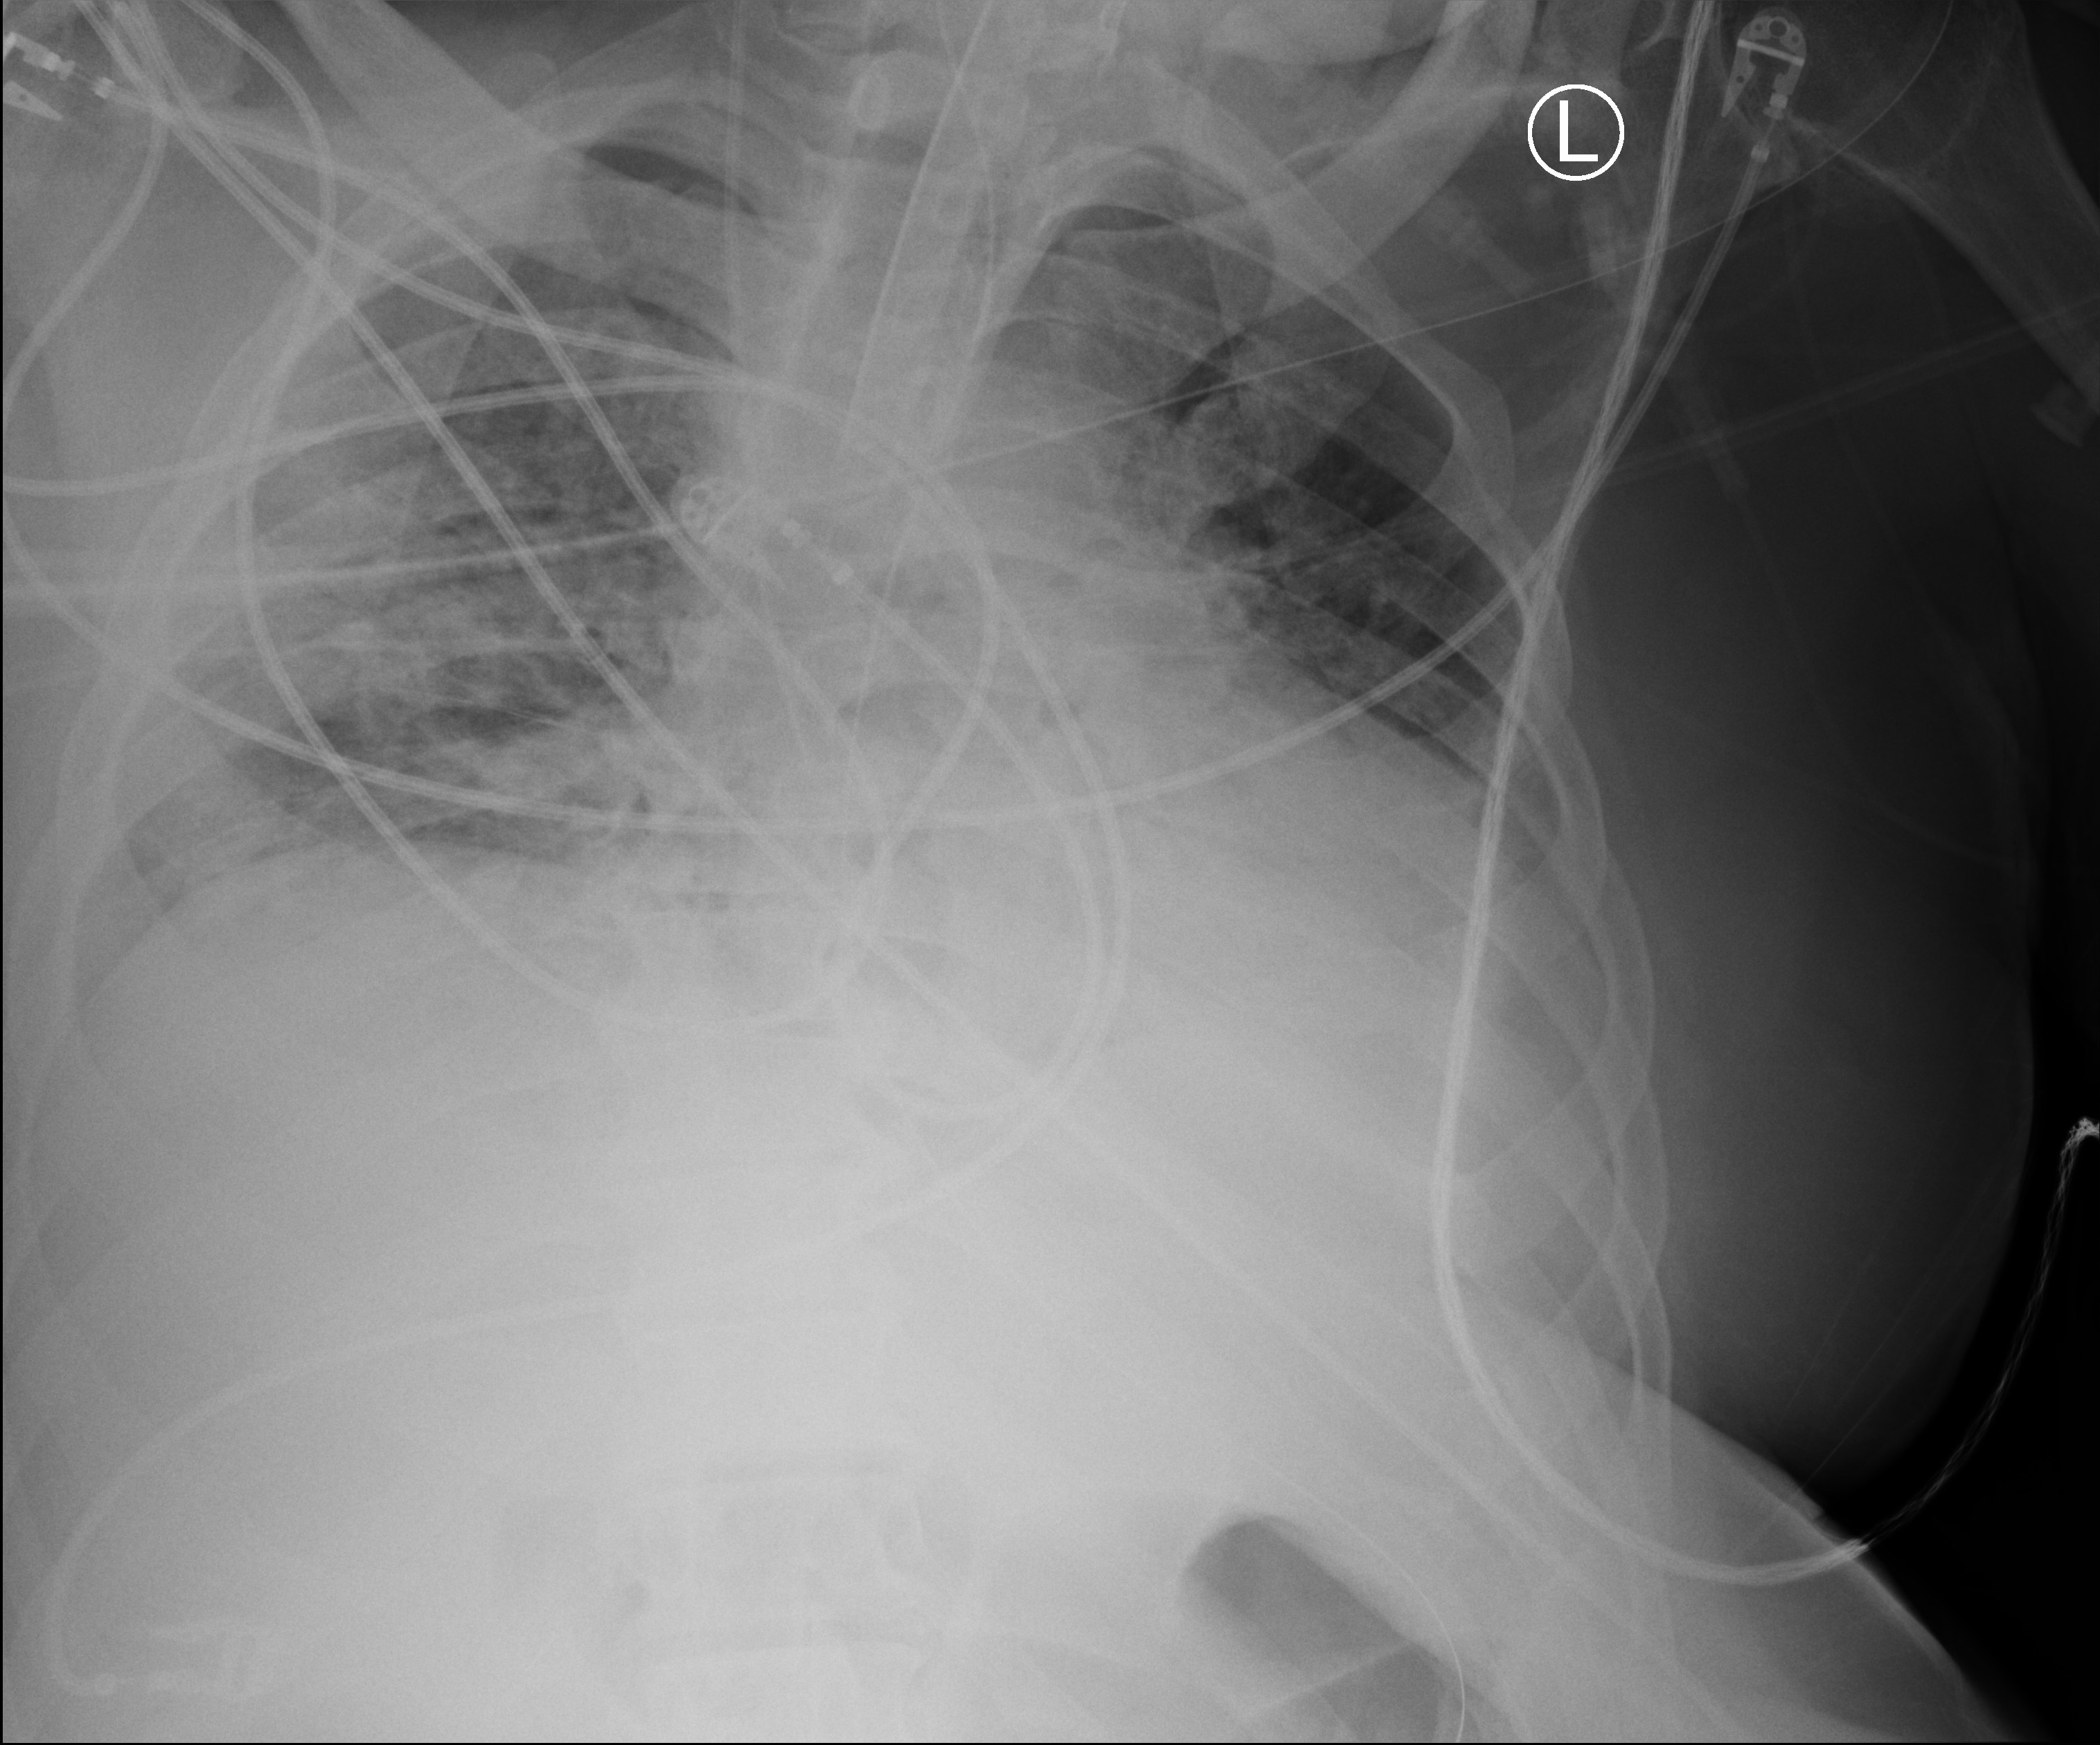
Bedside chest radiograph (computed radiography), anteroposterior (AP) projection. Male patient hospitalised with COVID-19, age 18–59 years.
Admission-level facts for this patient (not findings on this image; timing relative to this image not recorded): admitted to intensive care during this hospital stay: yes.